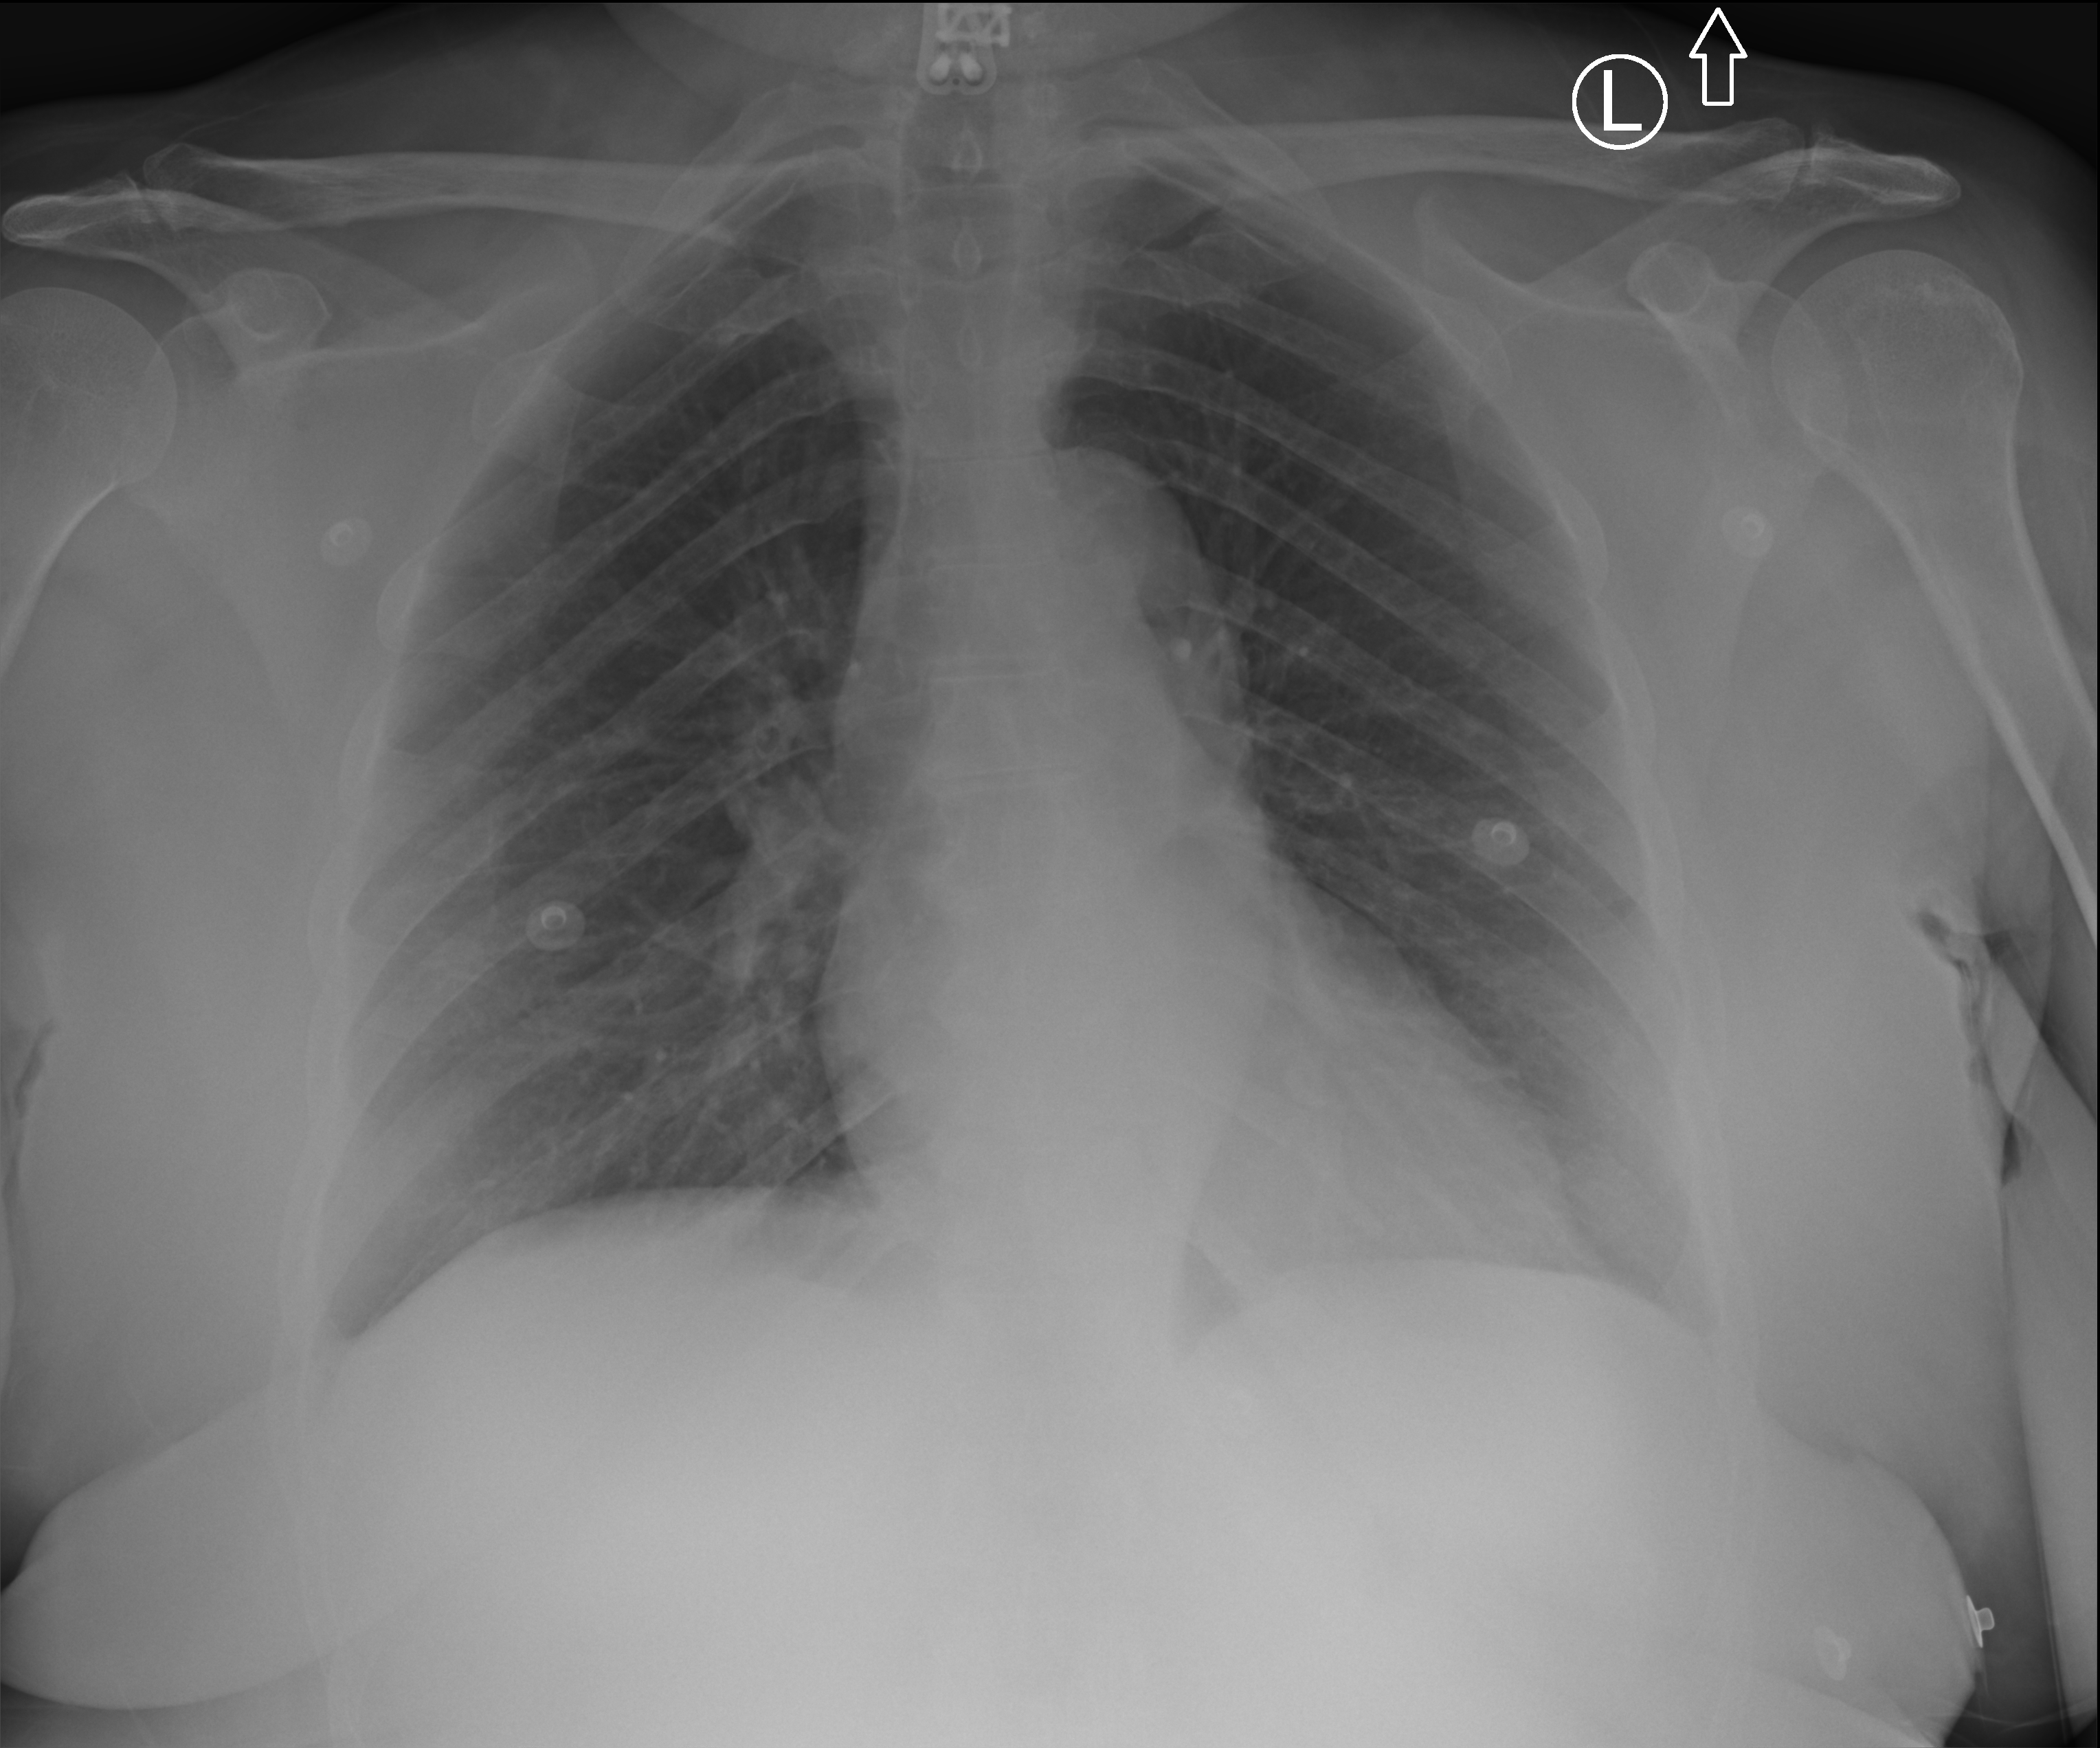
Chest radiograph; anteroposterior (AP) projection. Female patient hospitalised with COVID-19, age 60–74 years.
Hospital-stay facts (about this admission, not read from this image; timing relative to this image not recorded):
- admitted to intensive care during this hospital stay: no